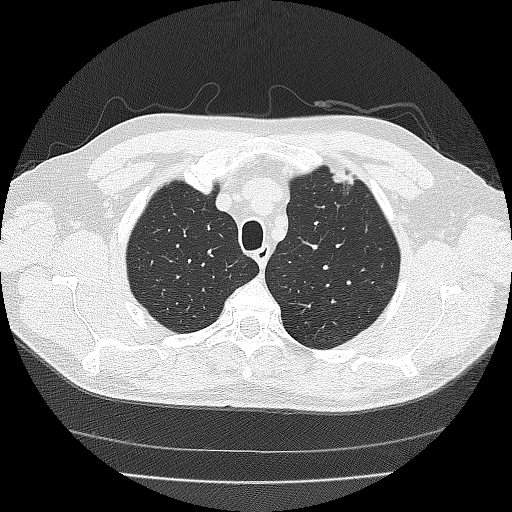
Low-dose screening chest CT, one axial slice; slice 134 of 167 in the series (ordered by position); lung window (W 1500 / L -600 HU); 2 mm slice thickness; 512 × 512 image matrix.
Outlined on this slice (expert manual segmentation):
- lesion 1 (tumor, upper lobe of left lung): bounding box [x1, y1, x2, y2] px = [330, 166, 354, 185]